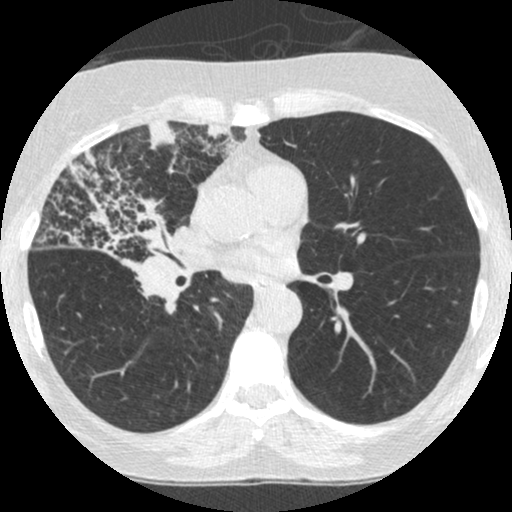
Low-dose screening chest CT, one axial slice. Reconstruction kernel STANDARD. 120 kVp. Lung window (W 1500 / L -600 HU). 1.25 mm slice thickness. 512 × 512 image matrix, field of view 294 × 294 mm.
Annotated regions visible in this slice (outlined manually by an expert reader):
- lesion 2 (tumor, hilum of right lung): box from (x=42, y=159) to (x=188, y=274) px
- lesion 3 (tumor, upper lobe of right lung): (x=148, y=121)–(x=177, y=153)
- lesion 4 (tumor, upper lobe of right lung): (x=203, y=124)–(x=242, y=159)